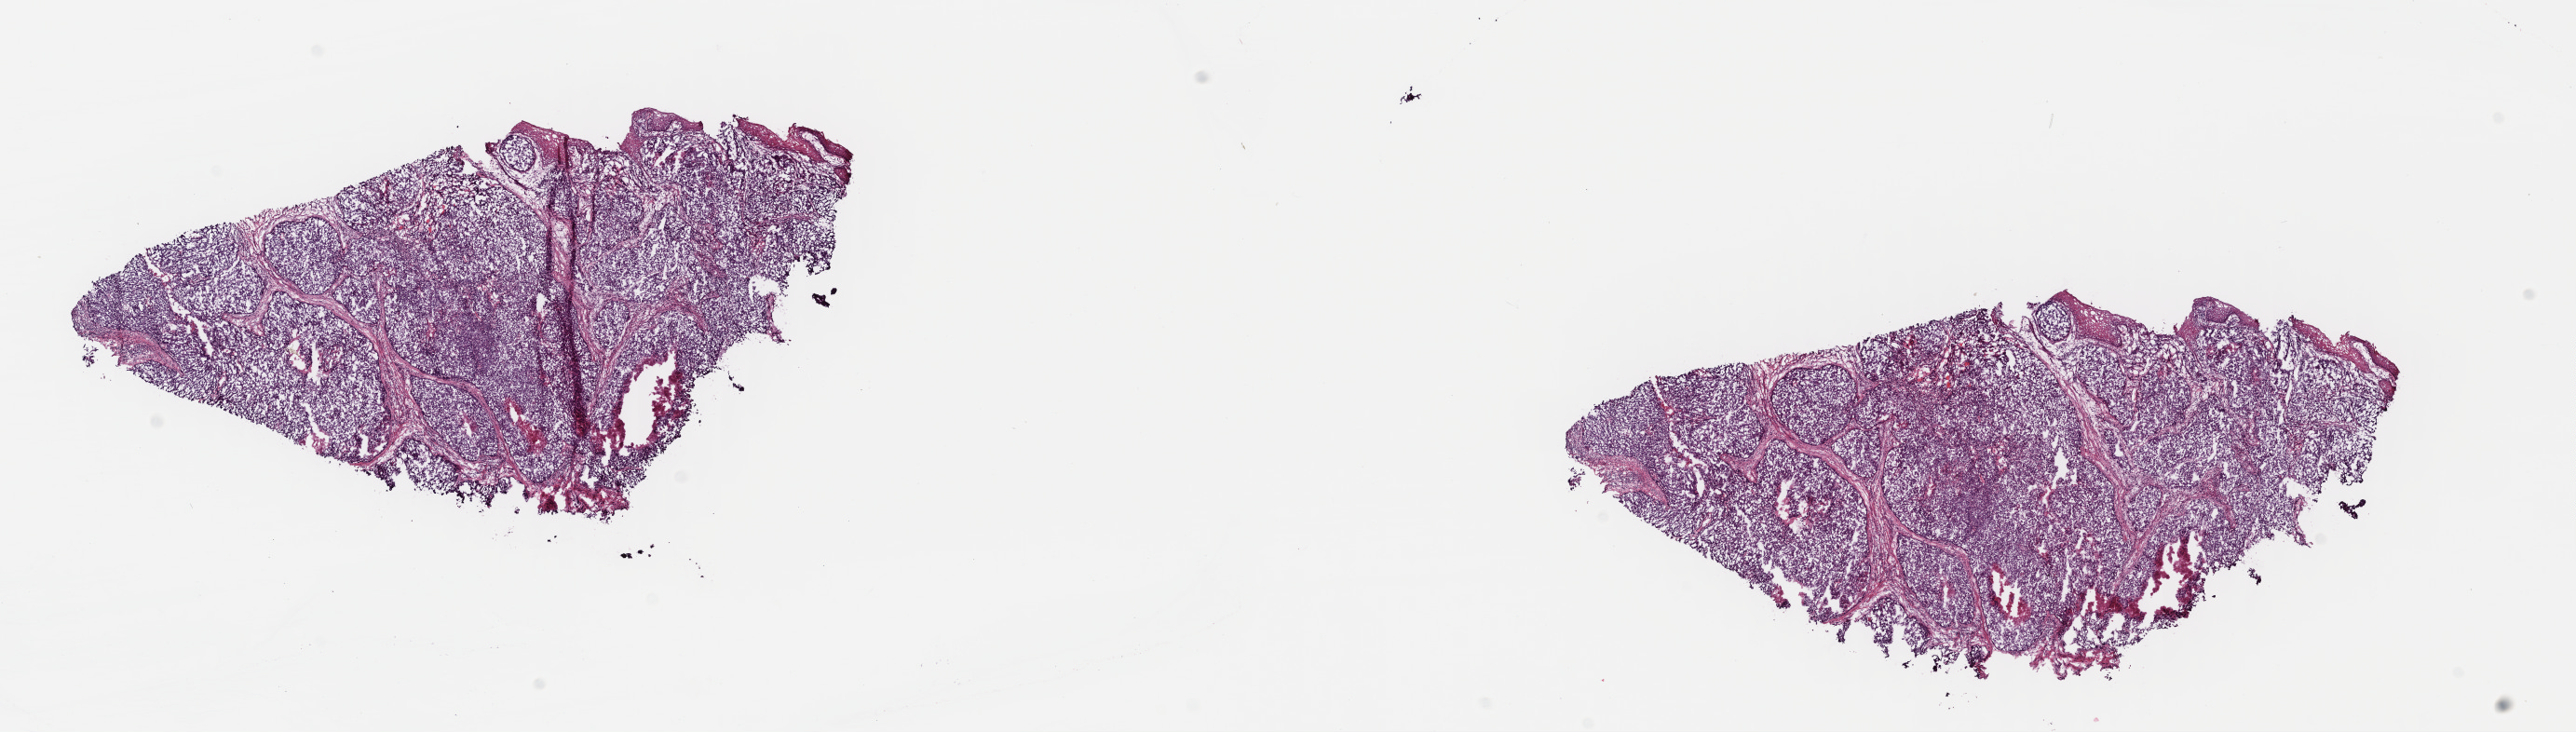
H&E-stained whole-slide image — whole scanned area (about 21.7 x 6.2 mm, from a 40x scan) shown as a low-resolution overview; frozen section from the top of the tissue portion; esophagus, primary tumour sample. Patient: female, age at initial diagnosis 69 years. Histologic grade: G2 (moderately differentiated). Pathologist review of this section (percent, as recorded): tumour cells 60%, tumour nuclei 88%, normal cells 5%, stromal cells 20%, necrosis 15%. Infiltration values recorded for this section: lymphocyte infiltration 4%, monocyte infiltration 1%, neutrophil infiltration 1%.
TNM: T3 N0 M0. Lymph nodes positive (case pathology): 0 of 2 examined. Histologic diagnosis: Squamous cell carcinoma, NOS. AJCC pathologic stage: IIB (7th edition).